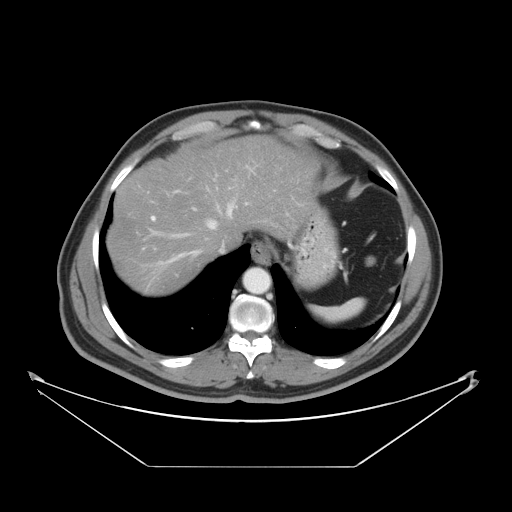
Contrast-enhanced abdominal CT, one axial slice. Slice 37 of 46 in the series (ordered by position). Reconstruction kernel STANDARD. 120 kVp. Intravenous contrast given. Soft-tissue window (W 400 / L 40 HU). 512 × 512 image matrix, field of view 465 × 465 mm. Male patient, age 57 years. Case-level facts recorded for this patient, not image findings: diagnosis: colorectal cancer liver metastases, imaged before liver resection; multiple liver metastases: no; largest metastasis: 3.3 cm; chemotherapy before resection: yes.
Annotated regions visible in this slice (outlined manually by an expert reader):
- hepatic veins: bounding box <169,198,248,262> (left, top, right, bottom; pixels)
- liver: <109,137,309,297>
- planned liver remnant (the part of the liver to remain after resection): <109,137,309,287>
- portal vein (with intrahepatic branches): <142,216,156,250>